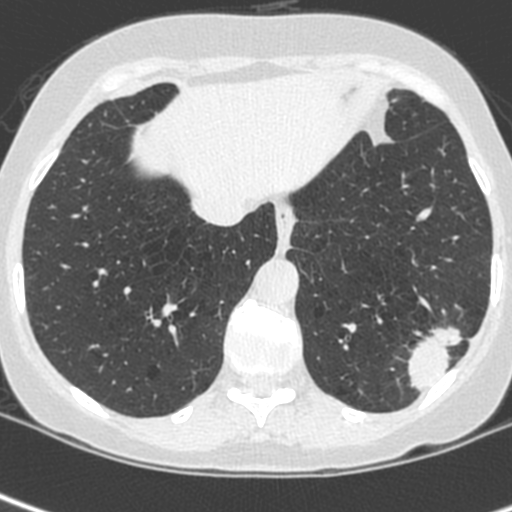
Axial slice from a low-dose chest CT screening exam. Baseline screening round. Lung window (W 1500 / L -600 HU). Slice 179 of 252 in the series. Female, age 56 years at enrolment.
- Expert-annotated lung lesion, bounding box (x1, y1, x2, y2) in pixels: (401, 307, 479, 386).
- Screening reader's record for this exam (one nodule recorded; not confirmed to be the boxed lesion): non-calcified nodule or mass ≥4 mm, left lower lobe, 37 × 29 mm, spiculated (stellate) margins, ground glass attenuation.
- Official screen result: positive, change unspecified: nodule(s) >= 4 mm or enlarging nodule(s), mass(es), or other non-specific abnormalities suspicious for lung cancer.
- Lung cancer was diagnosed 91 days after this screen: squamous cell carcinoma, NOS, left lower lobe, poorly differentiated (G3), stage IIIA (AJCC 6th edition), 35 mm at pathology.